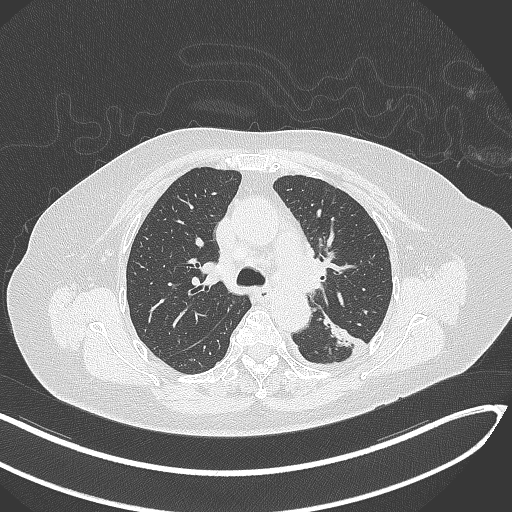
Chest CT, one axial slice; position 211 of 270 along the scan axis; lung window (W 1500 / L -600 HU); 512 × 512 image matrix, field of view 400 × 400 mm. Patient: female, 76 years. Case-level facts recorded for this patient, not image findings: clinical TNM (as recorded): T1c N0 M0.
Structures marked on this image (bounding box drawn by a radiologist):
- lung tumour (recorded histology: adenocarcinoma): box from (x=317, y=311) to (x=354, y=354) px